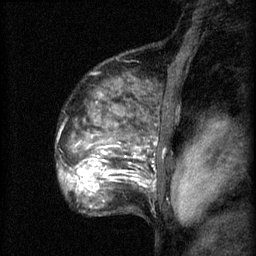
Breast MRI (dynamic contrast-enhanced), one sagittal slice; slice 48 of 60 in the series (ordered by position); 3 images stored at this slice position (order not interpretable as contrast timing); 1.5 T; TE 4.2 ms, TR 8.2 ms; 2 mm slice thickness; 256 × 256 image matrix, field of view 180 × 180 mm. Patient: female, 48 years.
Structures marked on this image (semi-automatic segmentation, software-assisted and operator-edited):
- analysis volume of interest (the breast-tissue region the enhancement analysis was run in; not a lesion): bounding box (x1, y1, x2, y2) in pixels: (61, 138, 153, 201)
- tumour enhancement mask (voxels above the 70 % enhancement threshold inside the analysis volume of interest): (61, 156, 145, 195)